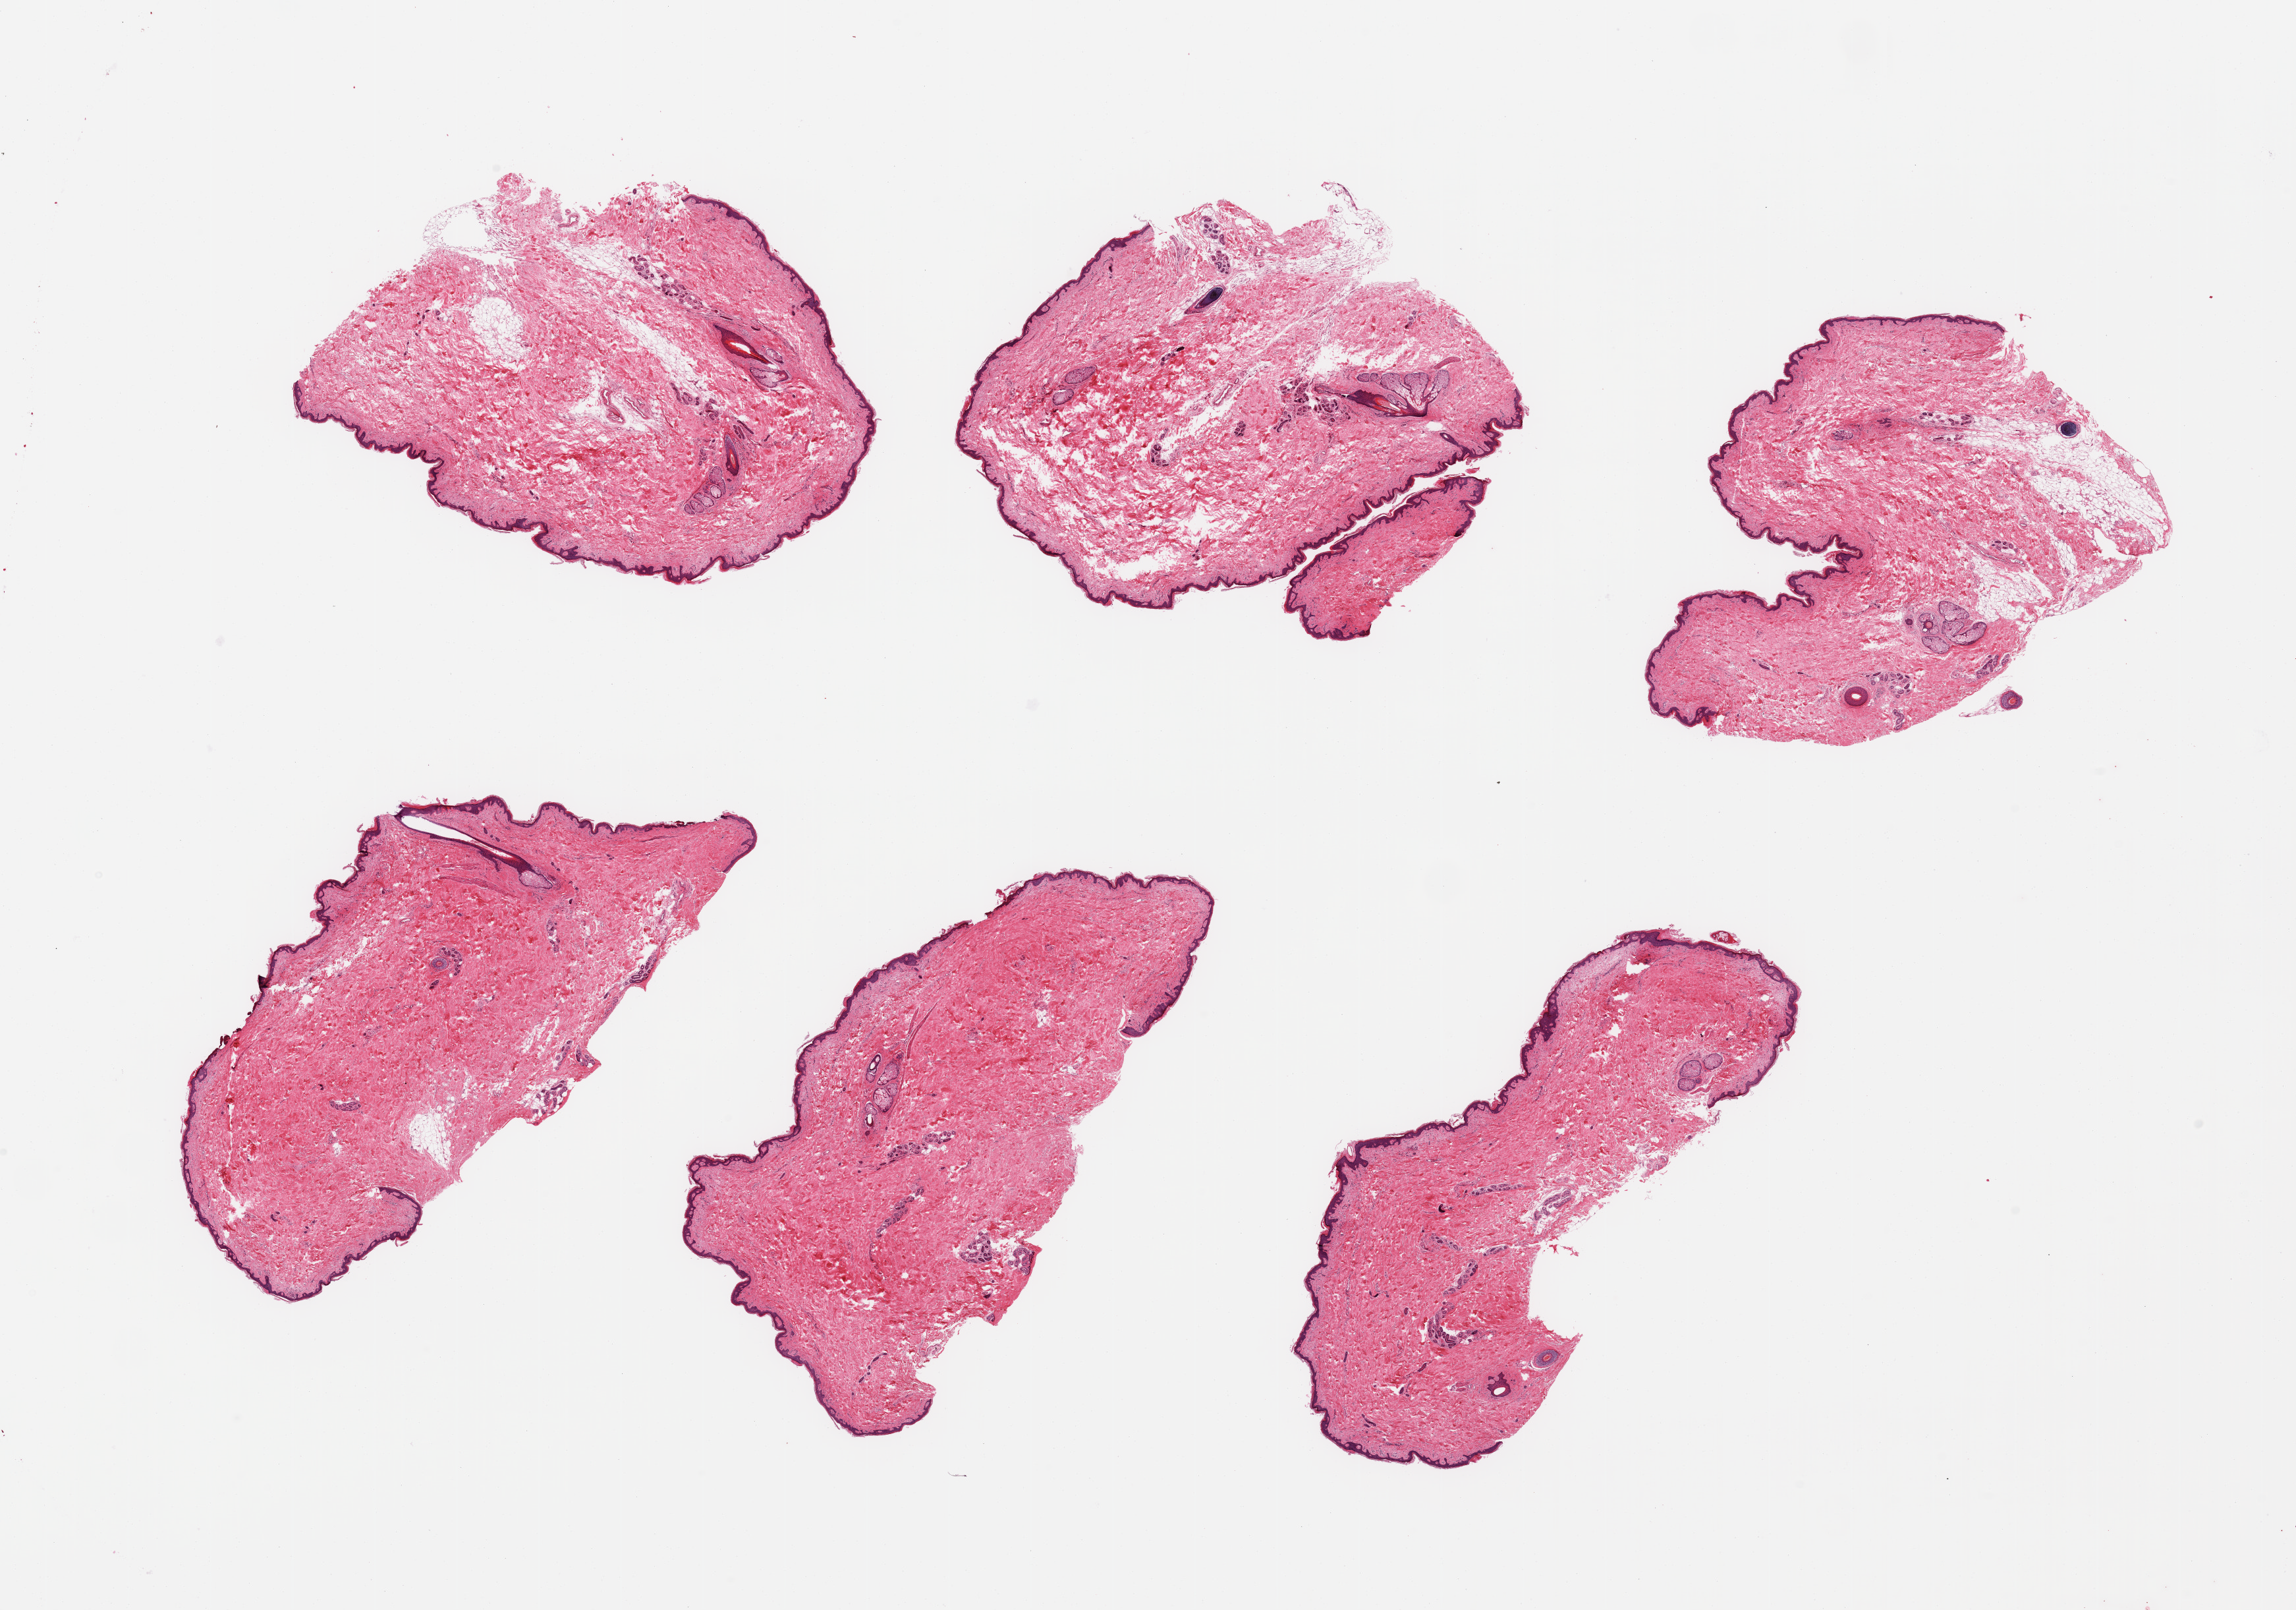
Hematoxylin and eosin (H&E) whole-slide image, whole scanned area (about 27.6 x 19.3 mm) shown as a low-resolution overview. PAXgene-fixed, paraffin-embedded tissue. Section of skin of suprapubic region (target tissue). Tissue donor sample. Male donor.
Review note (as recorded): 6 pieces, trace dermal fat; squamous epithelium is ~30-40 microns.